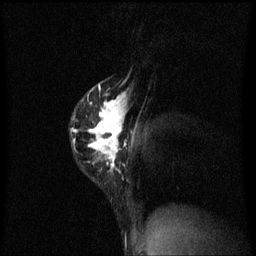
Breast MRI (dynamic contrast-enhanced), one sagittal slice. Slice 44 of 60 in the series (ordered by position). Dynamic contrast-enhanced series, image 2 of 3 at this slice position (ordered by acquisition). 1.5 T. TE 4.2 ms, TR 8.4 ms. 2 mm slice thickness. 256 × 256 image matrix, field of view 200 × 200 mm. Patient: female, 40 years.
Annotated regions visible in this slice (semi-automatic segmentation, software-assisted and operator-edited):
- analysis volume of interest (the breast-tissue region the enhancement analysis was run in; not a lesion): bounding box <71,76,130,183> (left, top, right, bottom; pixels)
- tumour enhancement mask (voxels above the 70 % enhancement threshold inside the analysis volume of interest): <71,84,128,171>